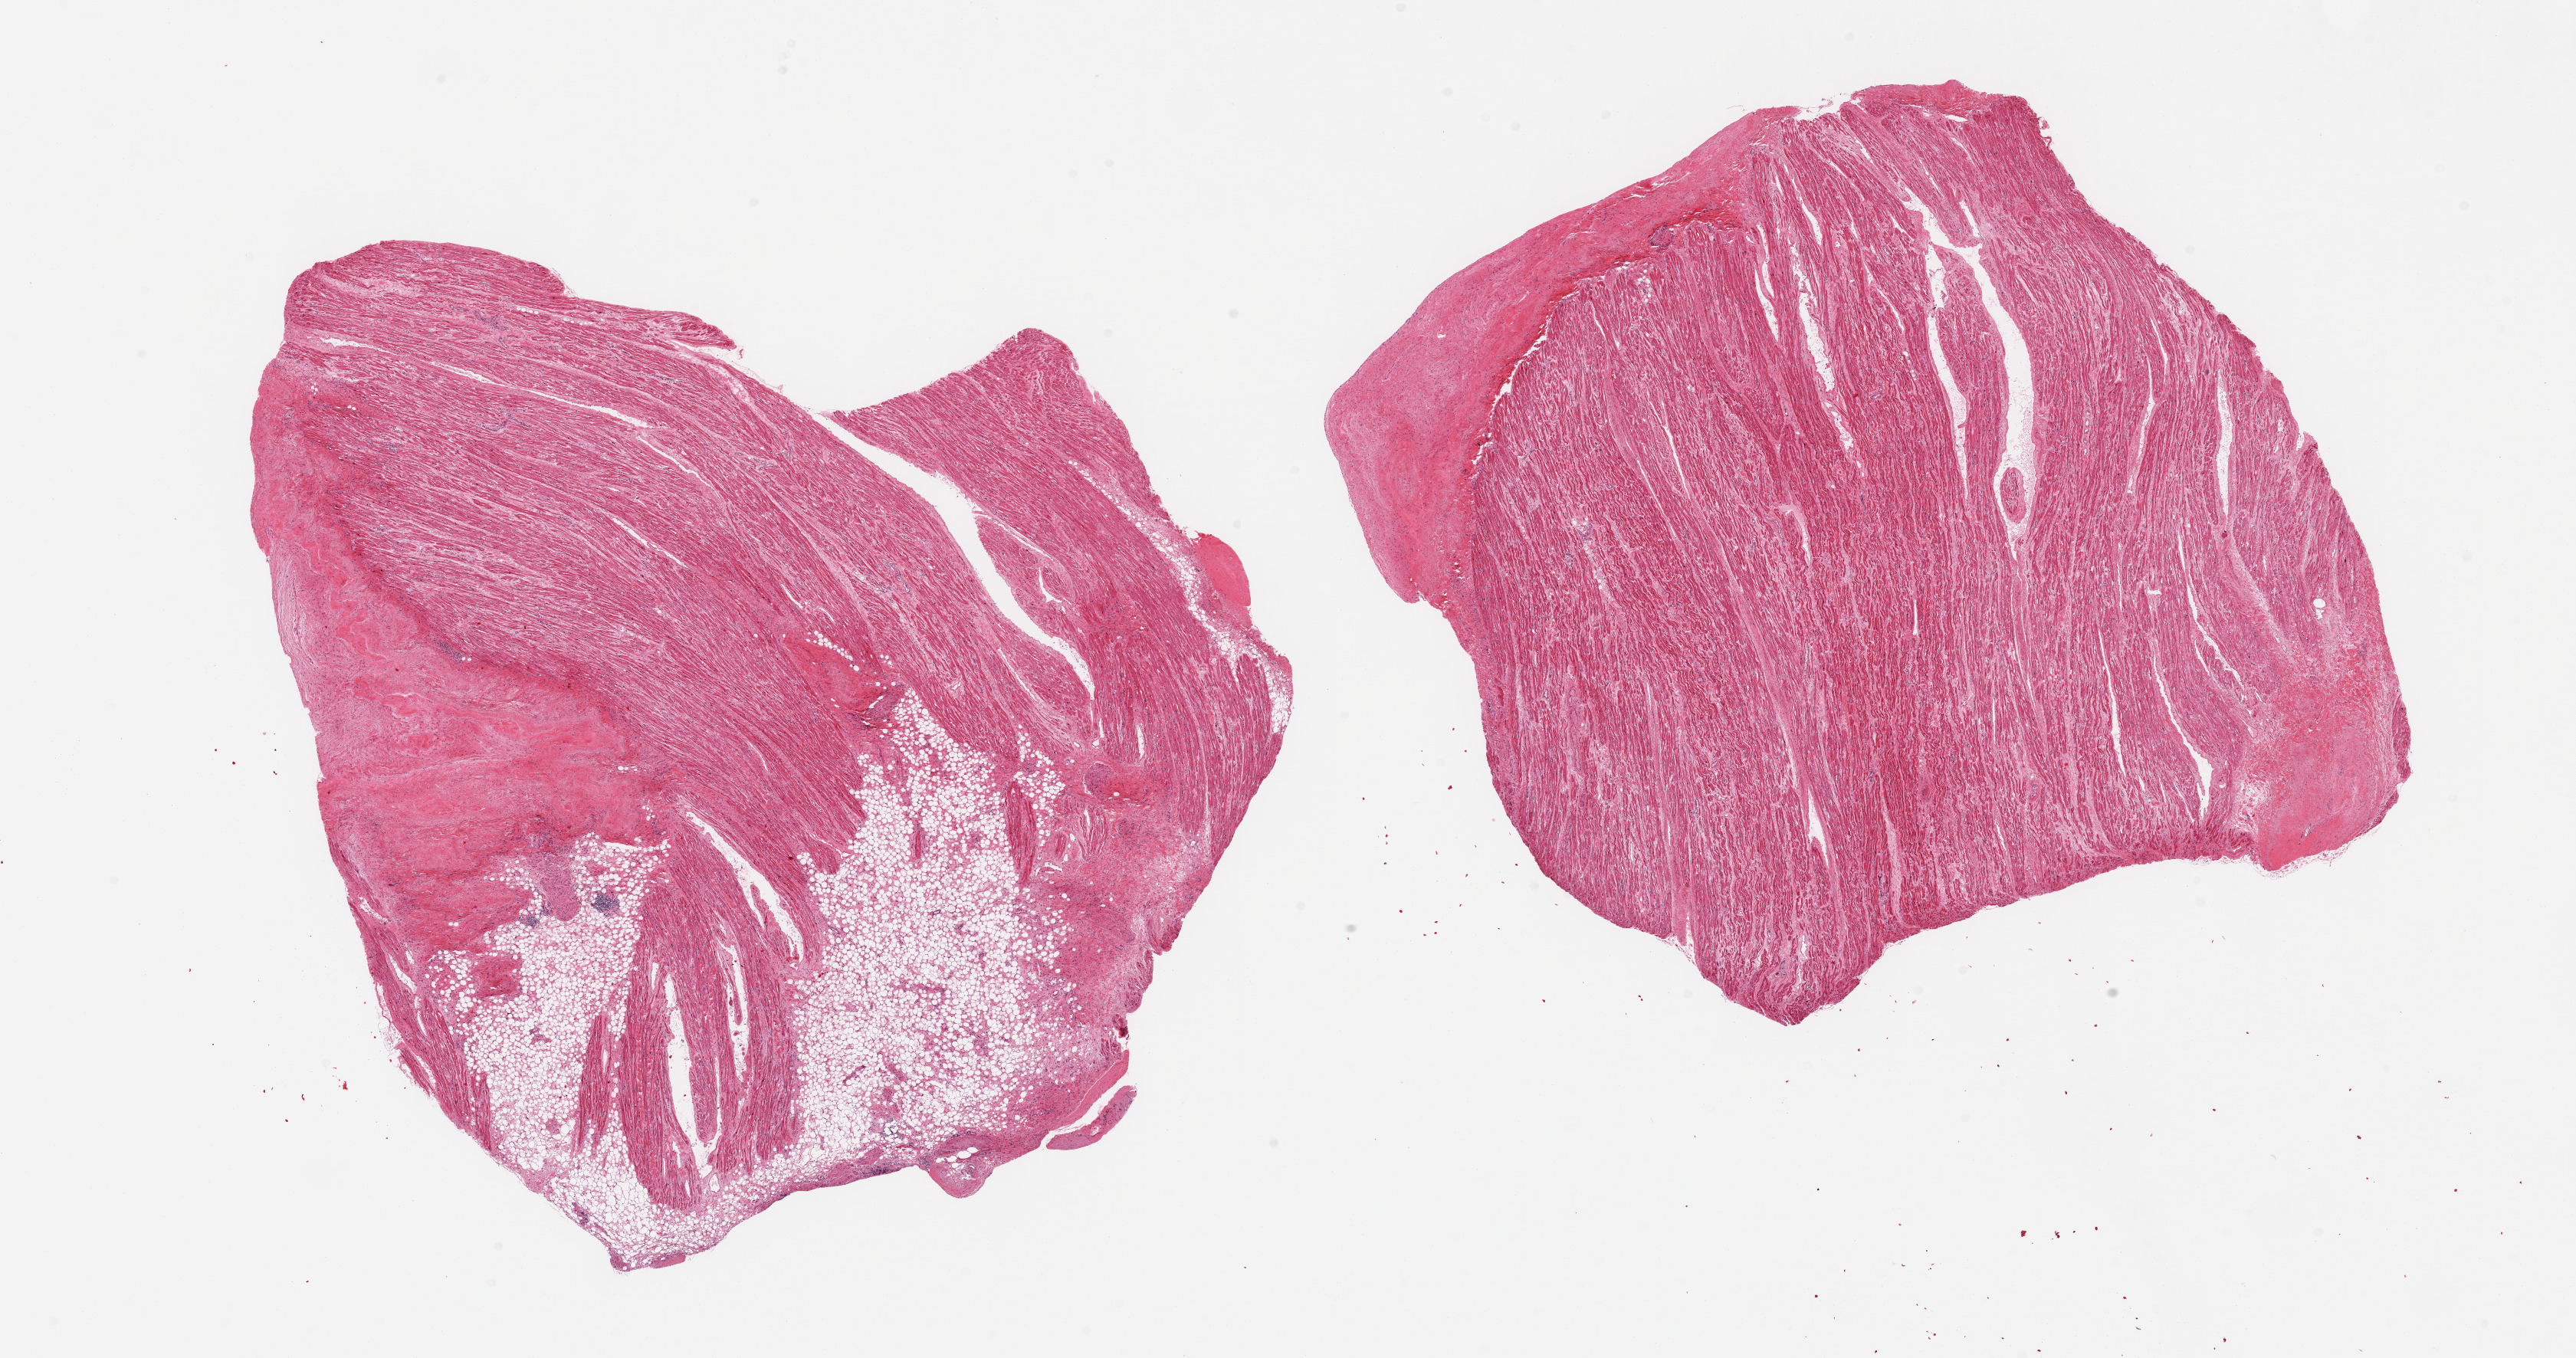
Whole-slide image, H&E stain — shown as a low-resolution overview of the whole scanned area (about 26.6 x 14.0 mm); PAXgene-fixed paraffin-embedded (PFPE) section; target tissue: auricular appendage; tissue donor sample. Donor sex: male.
Reviewer comment on this tissue sample: 2 pieces; High (60%) peripheral fibrofatty content on 1, and 10% peripheral fibrous content on other.